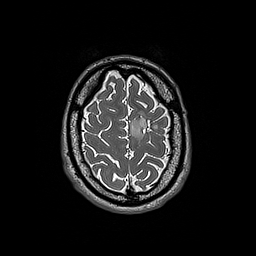
Brain MRI from a brain-tumour surgery series, one axial slice. 1 mm slice thickness. 256 × 256 image matrix, field of view 250 × 250 mm. Case-level facts recorded for this patient, not image findings: histopathology: Oligodendroglioma; WHO grade: 3; IDH mutation: yes.
Structures marked on this image (outlined manually by an expert reader):
- tumour: bounding box (x1, y1, x2, y2) in pixels: (130, 113, 158, 144)